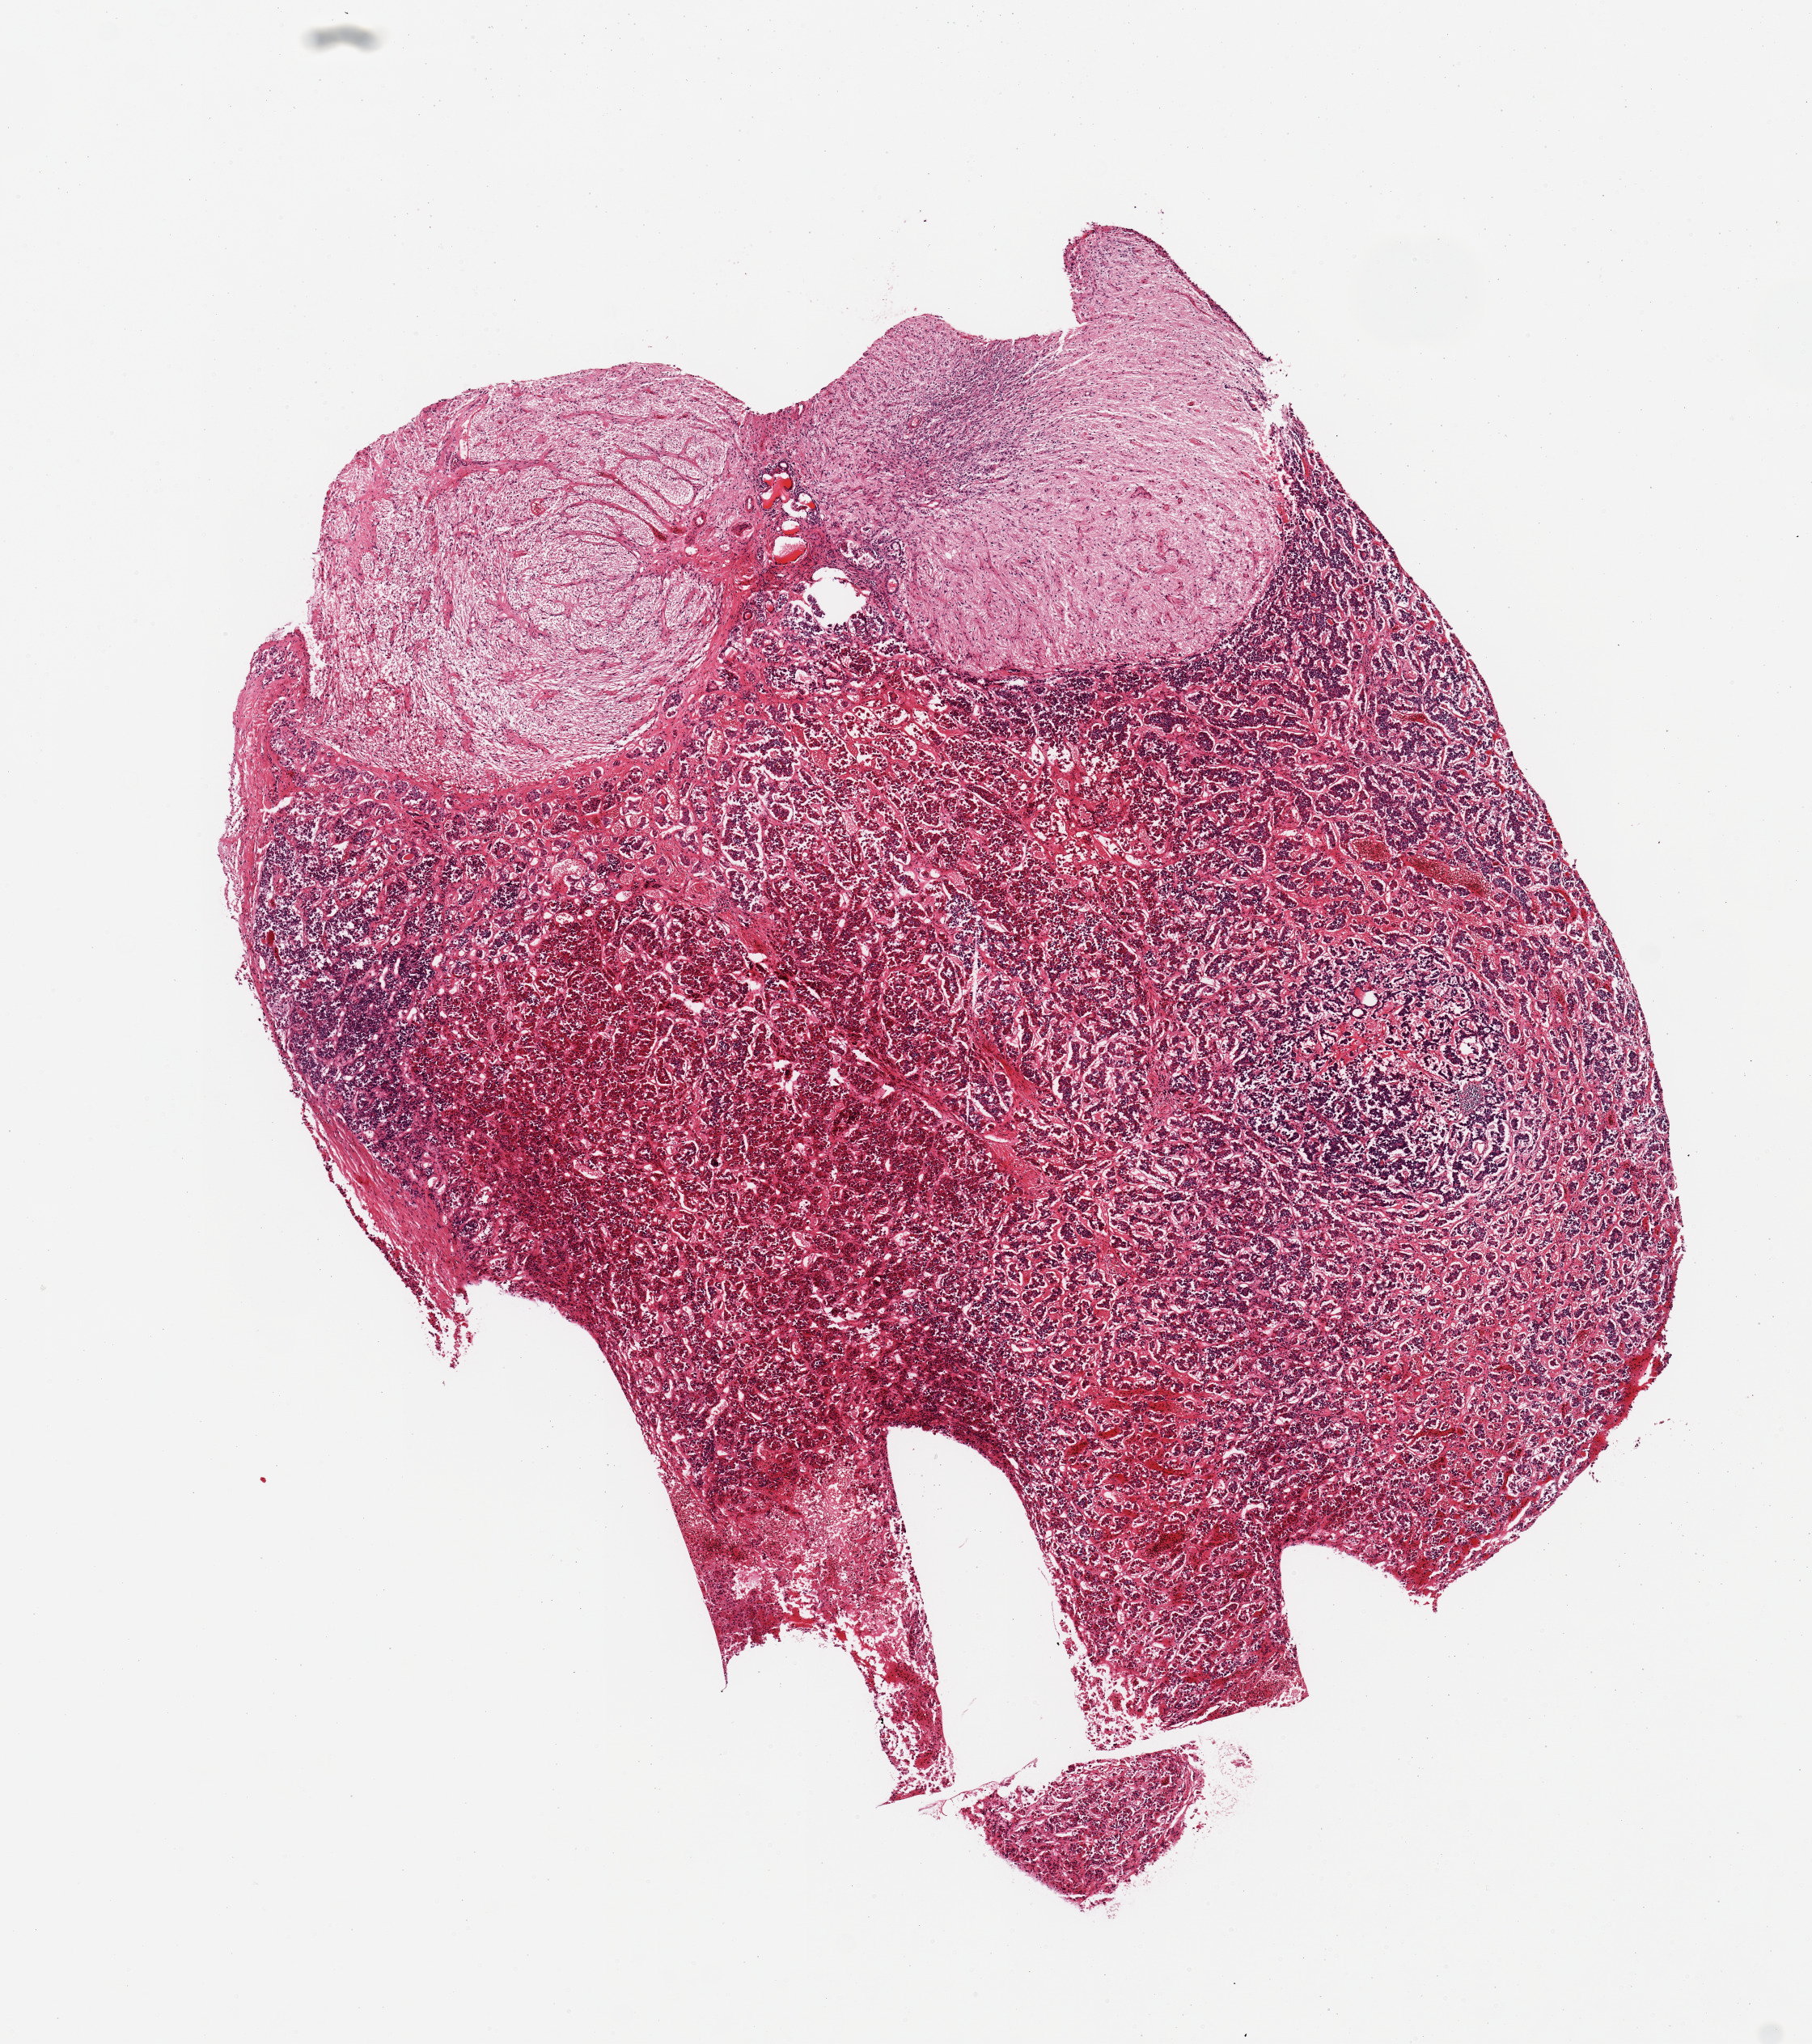
Digitized hematoxylin and eosin (H&E)-stained section — whole scanned area (about 8.9 x 10.0 mm) shown as a low-resolution overview. PAXgene-fixed, paraffin-embedded tissue. Sampled site (target tissue): pituitary. Tissue donor sample. Donor sex: female.
Reviewer comment on this tissue sample: 1 piece, prominent adenohypophysis, 4mm neurohypophysis.